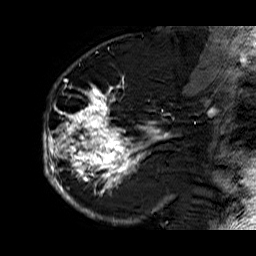
Breast MRI (dynamic contrast-enhanced), one sagittal slice; slice 39 of 60 in the series (ordered by position); dynamic contrast-enhanced series, time point 2 of 6 at this slice position (early post-contrast); 1.5 T; TE 6.3 ms, TR 32.9 ms; 4 mm slice thickness; 256 × 256 image matrix, field of view 200 × 200 mm. Female patient. From the clinical record (not read from this slice): setting: breast cancer imaged before/during neoadjuvant chemotherapy; receptor status: HR-positive, HER2-negative.
Outlined on this slice (semi-automatically segmented with operator editing):
- analysis volume of interest (the breast-tissue region the enhancement analysis was run in; not a lesion): bounding box (x1, y1, x2, y2) in pixels: (43, 74, 176, 210)
- tumour enhancement mask (voxels above the 100 % enhancement threshold inside the analysis volume of interest): (43, 74, 174, 210)